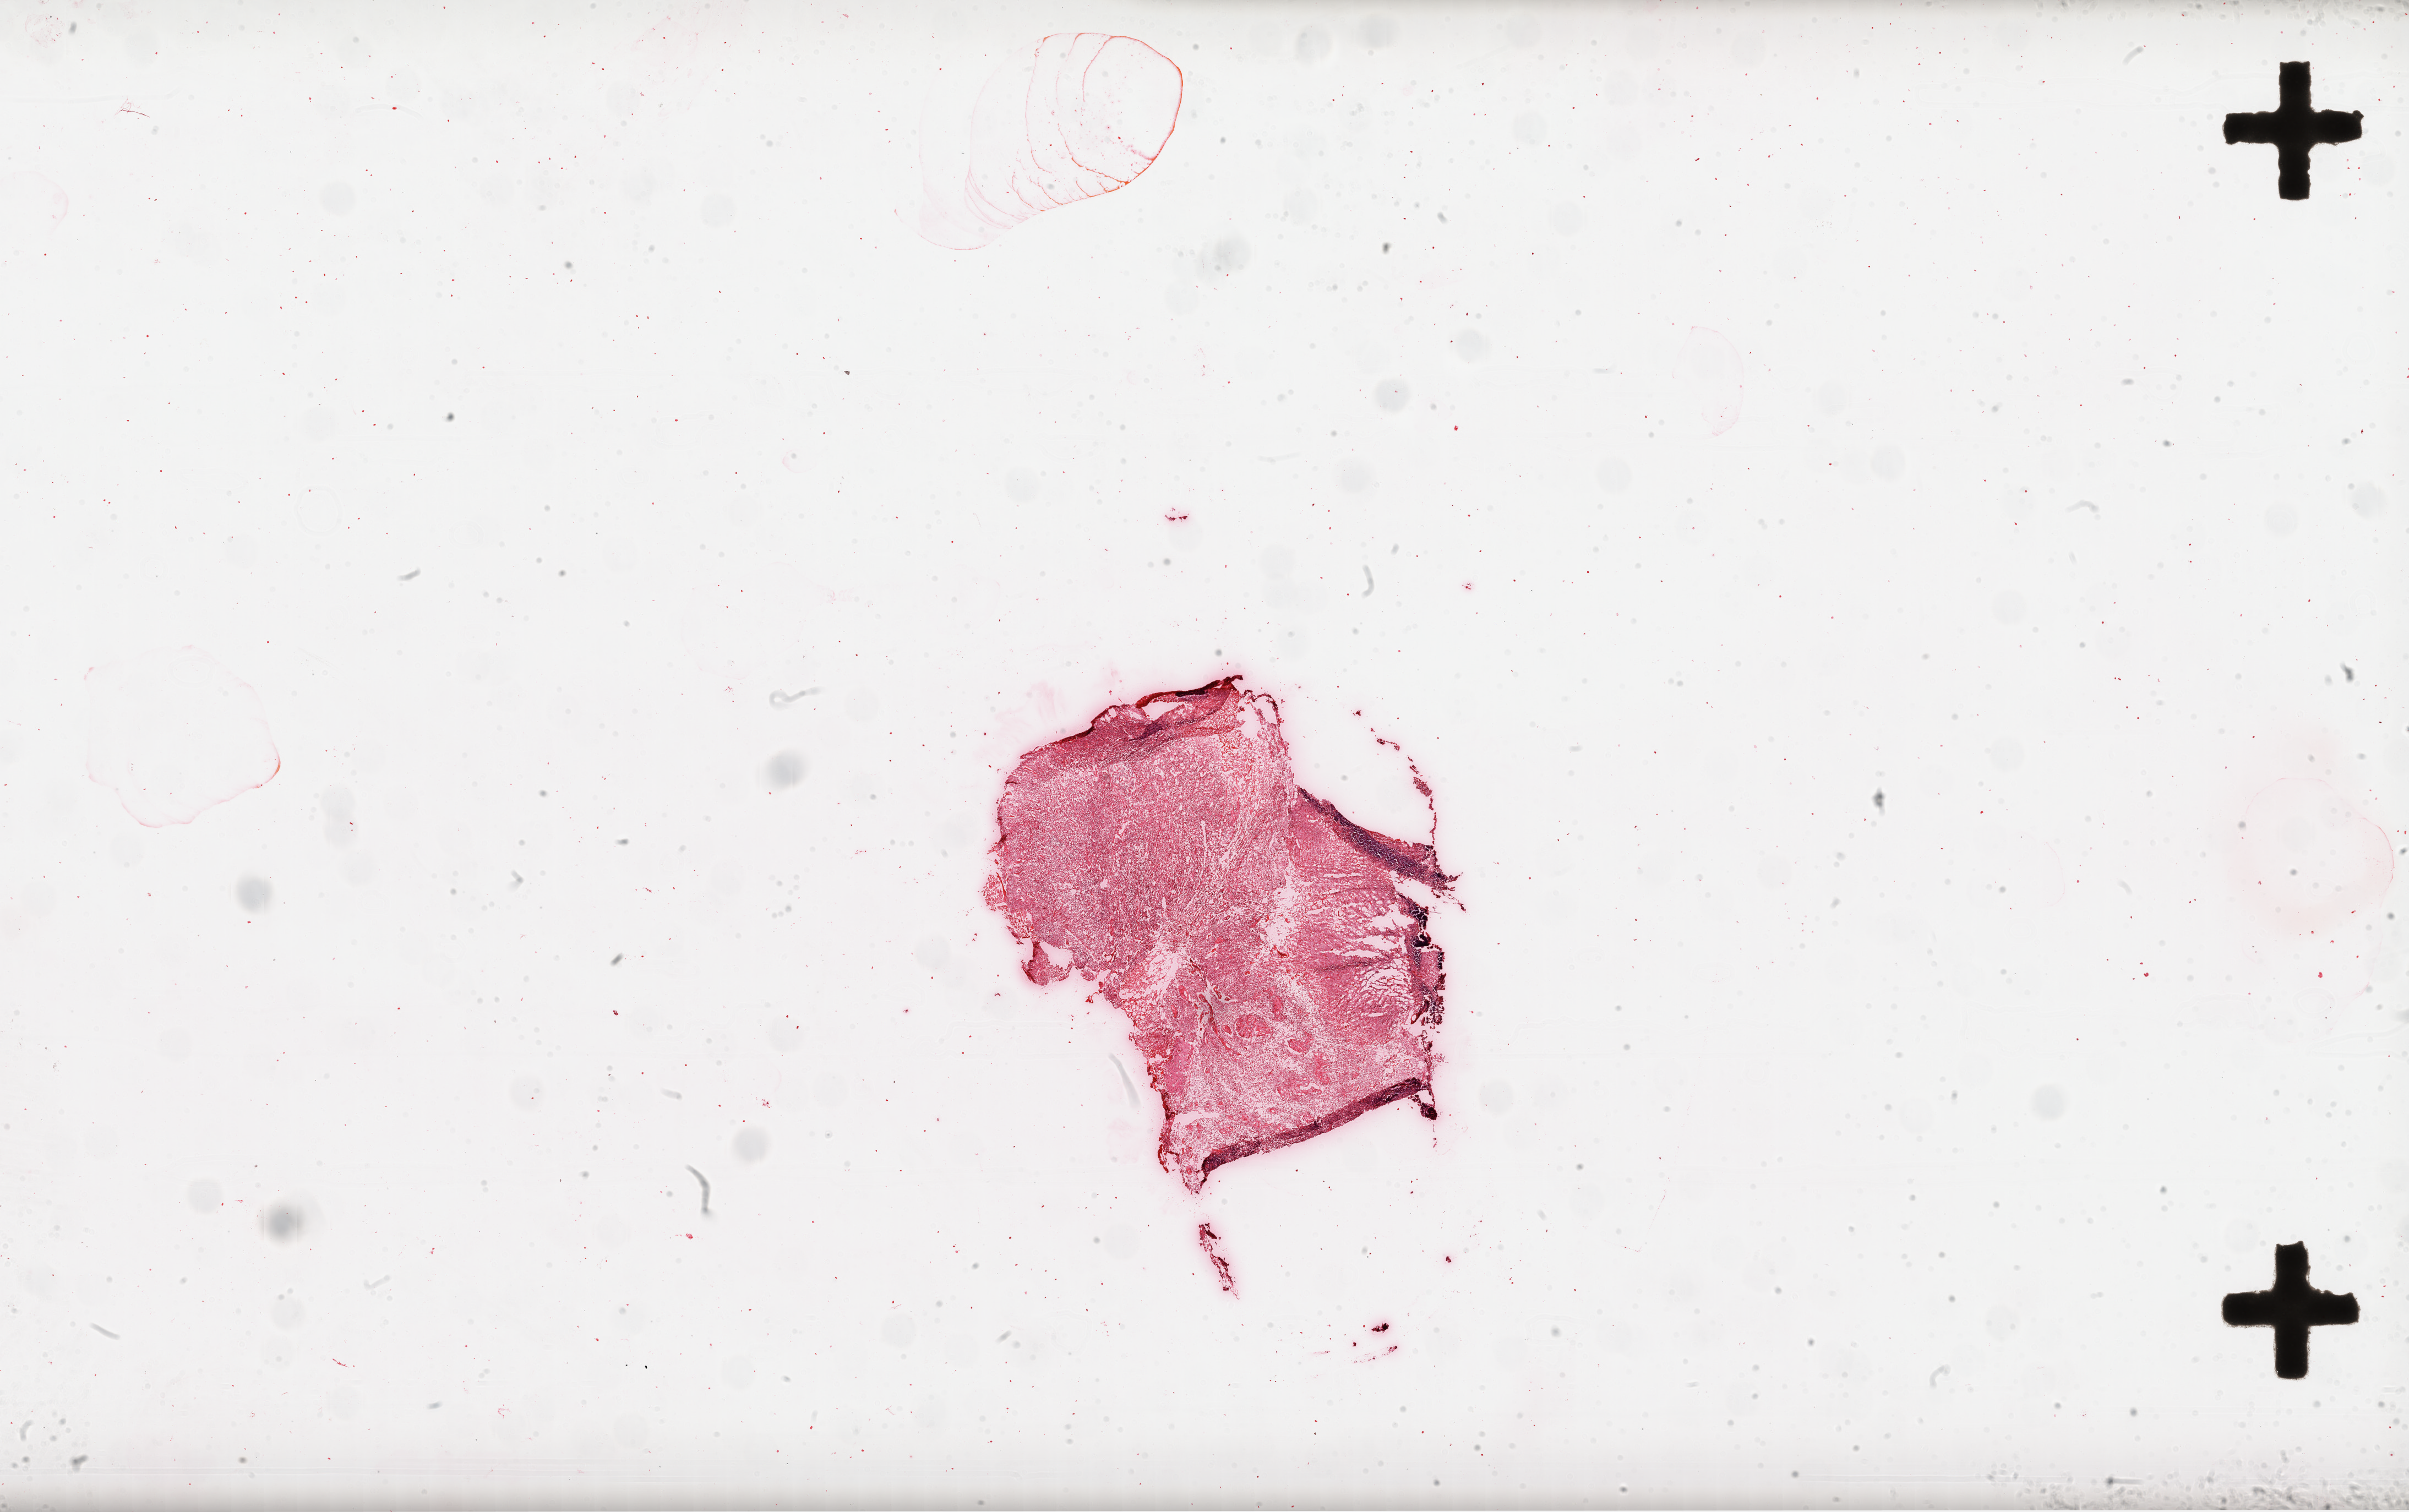
H&E whole-slide image — low-resolution overview of the scanned area, about 35.3 x 22.2 mm; frozen section from the top of the tissue portion; sample: primary tumour, brain. Female patient; age at initial diagnosis 66 years. Composition of this section per pathologist review: tumour cells 85%, tumour nuclei 100%, normal cells 0%, stromal cells 0%, necrosis 15%.
Histologic diagnosis: Glioblastoma.